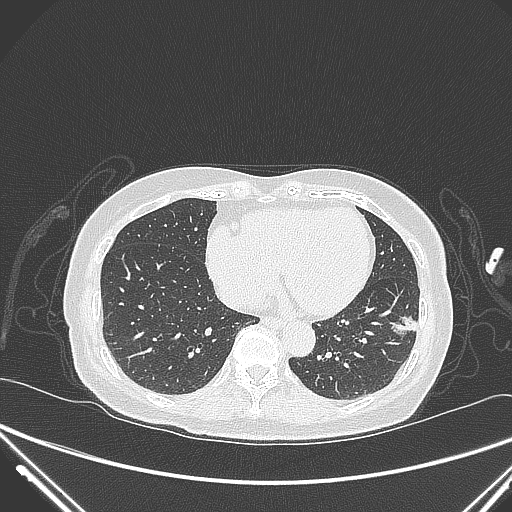
Chest CT, one axial slice; 120 kVp; lung window (W 1500 / L -600 HU); 1 mm slice thickness; 512 × 512 image matrix, field of view 377 × 377 mm. Female patient, age 82 years. From the clinical record (not read from this slice): clinical TNM (as recorded): T1c N0 M0.
Annotated regions visible in this slice (bounding box drawn by a radiologist):
- lung tumour (recorded histology: adenocarcinoma): bounding box [x1, y1, x2, y2] px = [387, 306, 422, 348]